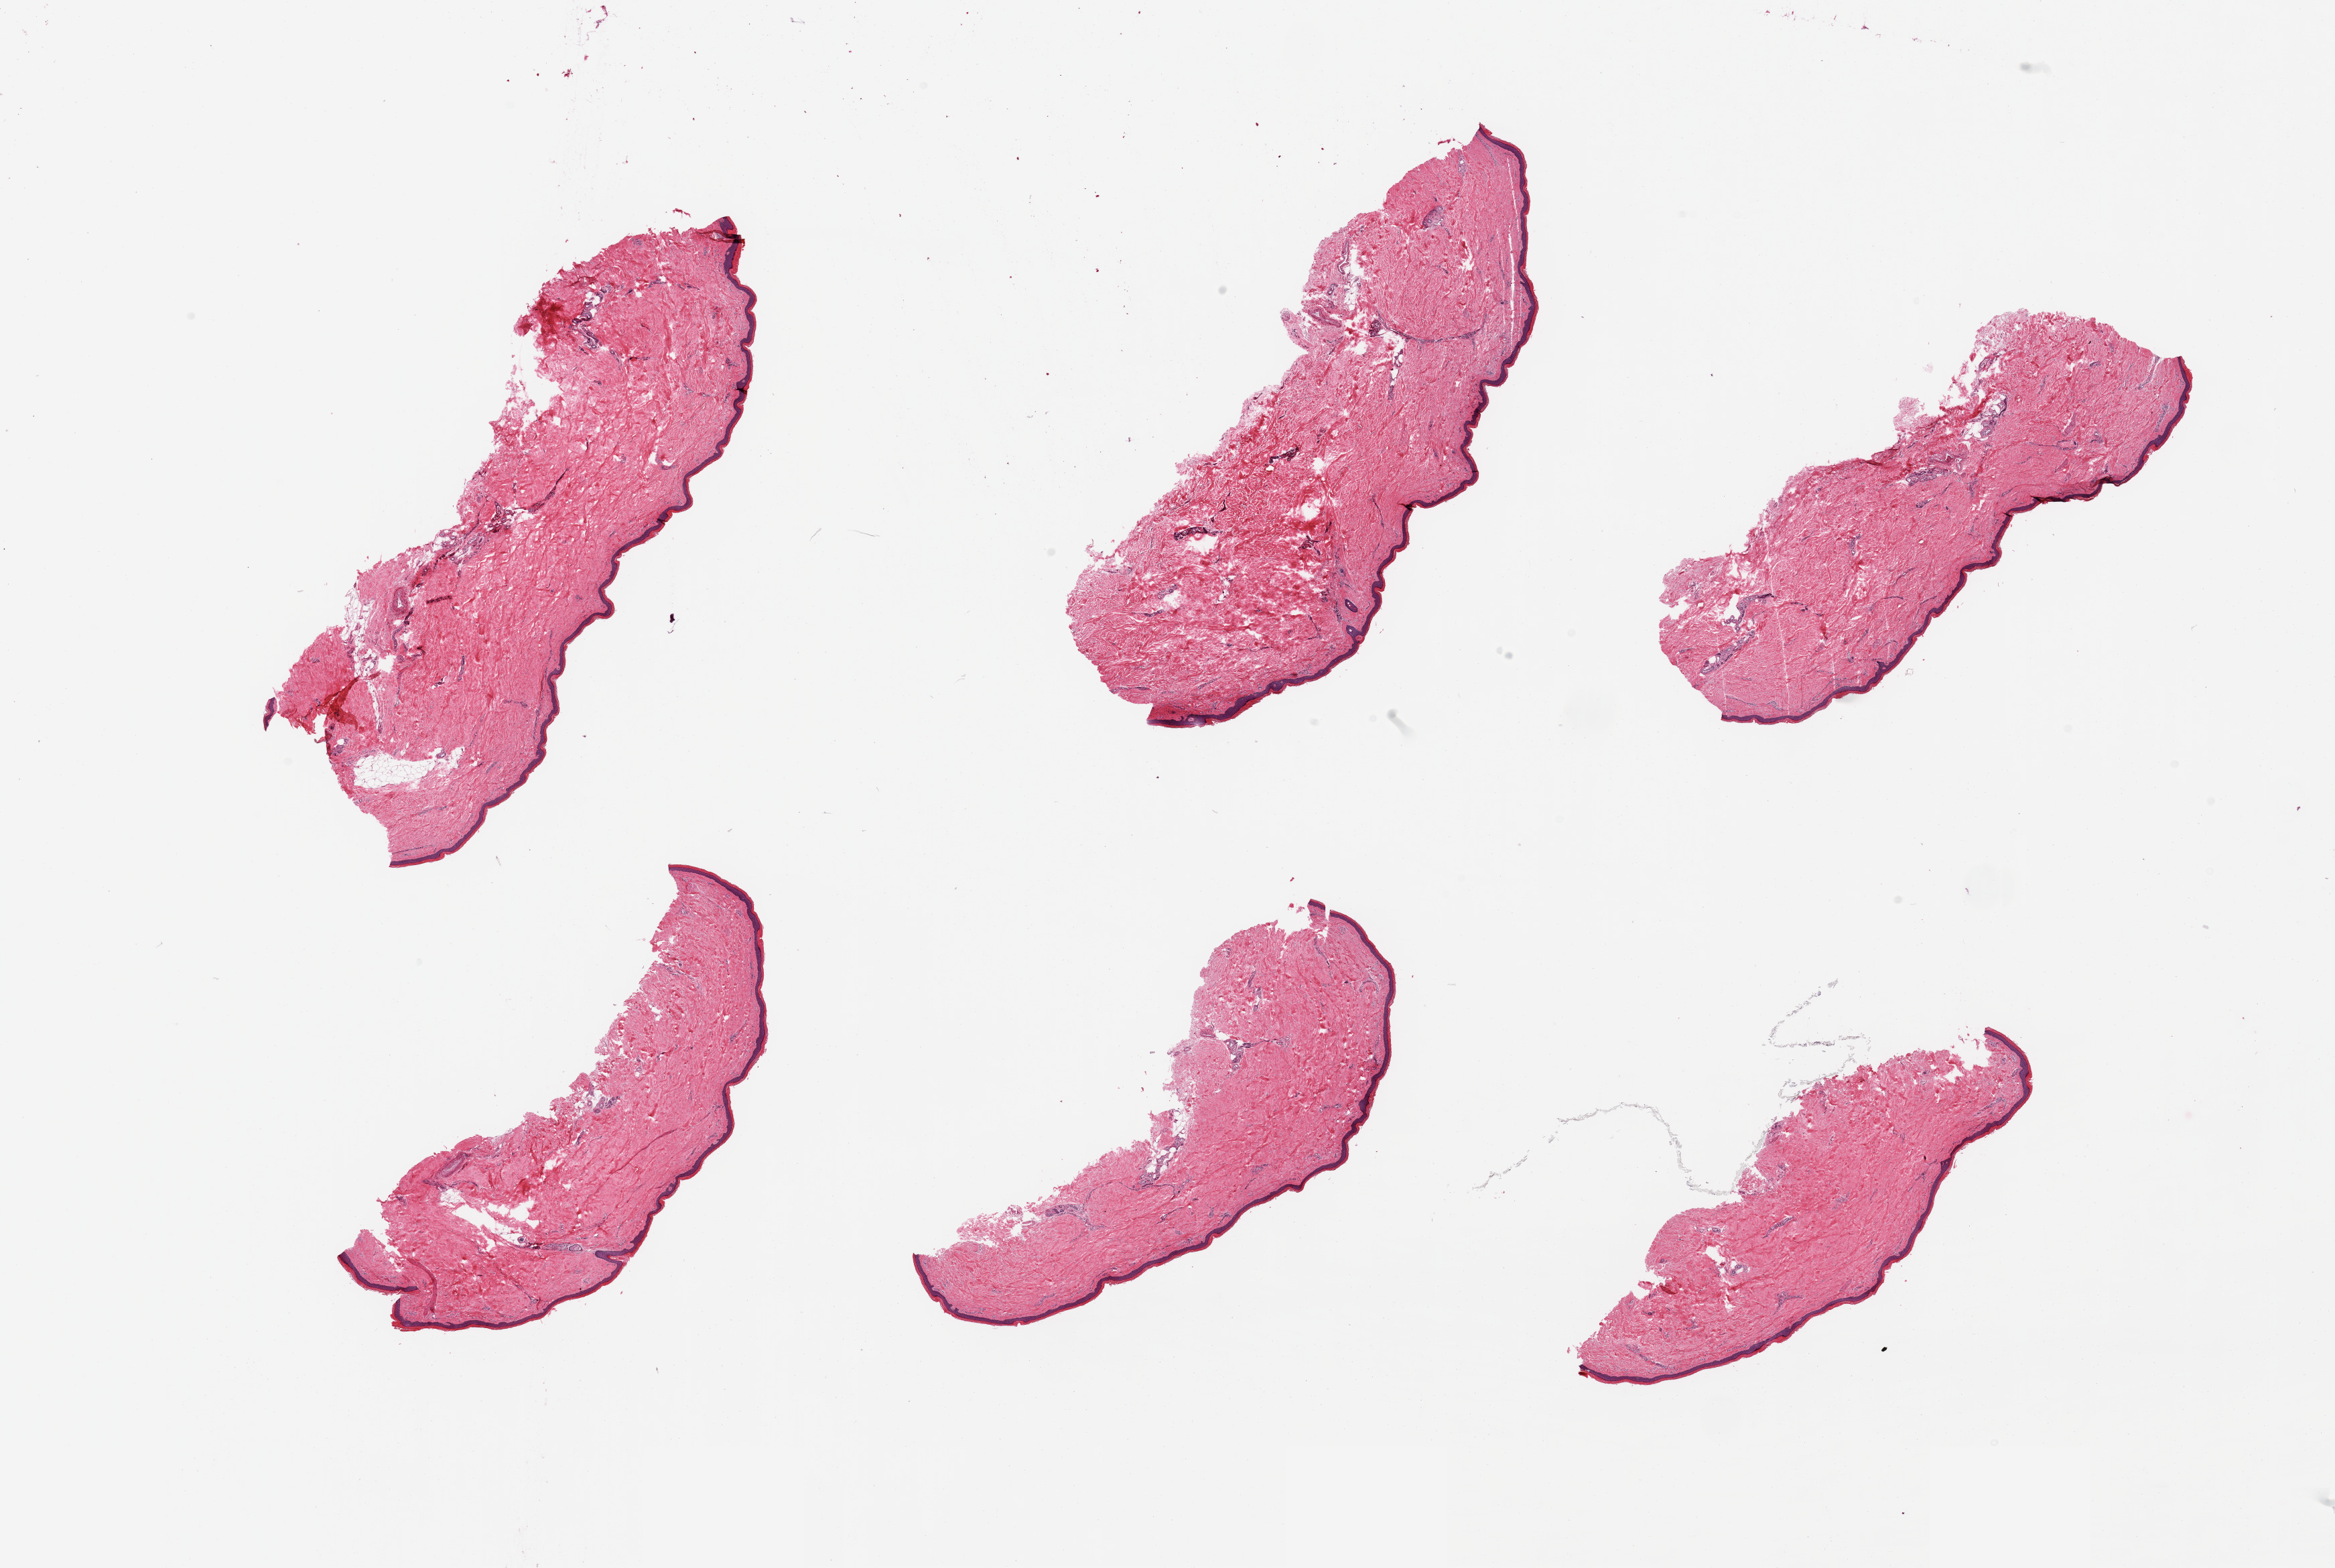
Whole-slide image, haematoxylin and eosin stain, brightfield, shown as a low-resolution overview of the whole scanned area (about 27.6 x 18.5 mm, acquisition: 20x scan). PAXgene-fixed paraffin-embedded (PFPE) section. Sampled site (target tissue): skin of lower leg. Donor tissue sample. Donor: male.
Reviewer comment on this tissue sample: 6 pieces; well trimmed; <5% dermal fat.